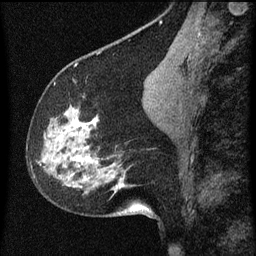
Breast MRI (dynamic contrast-enhanced), one sagittal slice; position 28 of 60 along the scan axis; dynamic contrast-enhanced series, image 2 of 3 at this slice position (ordered by acquisition); 1.5 T; TE 4.2 ms, TR 8 ms; 2 mm slice thickness; 256 × 256 image matrix, field of view 180 × 180 mm. Patient: female, 61 years.
Structures marked on this image (semi-automatically segmented with operator editing):
- analysis volume of interest (the breast-tissue region the enhancement analysis was run in; not a lesion): bounding box [x1, y1, x2, y2] px = [27, 80, 139, 209]
- tumour enhancement mask (voxels above the 70 % enhancement threshold inside the analysis volume of interest): [74, 118, 95, 161]